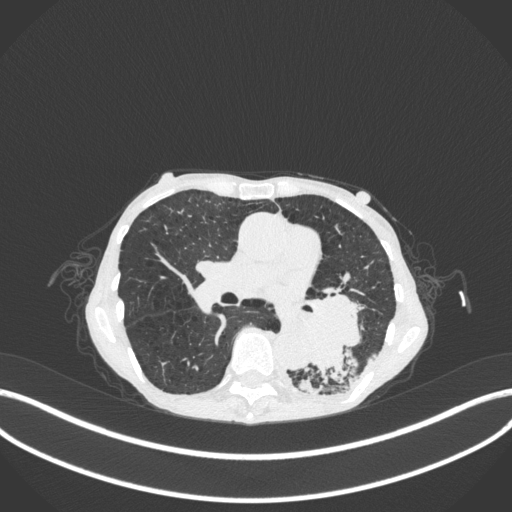
Chest CT, one axial slice. Slice 143 of 347 in the series (ordered by position). Reconstruction kernel B31f. 120 kVp. Lung window (W 1500 / L -600 HU). 1 mm slice thickness. 512 × 512 image matrix, field of view 400 × 400 mm. Patient: female, 70 years. From the clinical record (not read from this slice): clinical TNM (as recorded): T3 N0 M0.
Outlined on this slice (rectangle marked by the reading radiologist):
- lung tumour (recorded histology: small cell carcinoma): bounding box (x1, y1, x2, y2) in pixels: (292, 286, 368, 375)